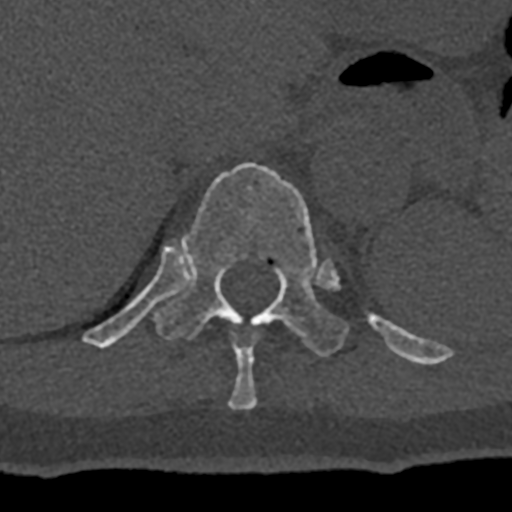
CT including the spine, one axial slice; position 559 of 797 along the scan axis; 120 kVp; bone window (W 1800 / L 400 HU); 0.5 mm slice thickness; 512 × 512 image matrix. Patient: male, 74 years. Case-level facts recorded for this patient, not image findings: primary cancer: renal; vertebrae with lytic lesions (as recorded): T10, L1, L2, L3, L4, L5.
Outlined on this slice (semi-automatically segmented with operator editing):
- T10 vertebra: bounding box (x1, y1, x2, y2) in pixels: (228, 332, 258, 409)
- T11 vertebra: (82, 163, 432, 365)